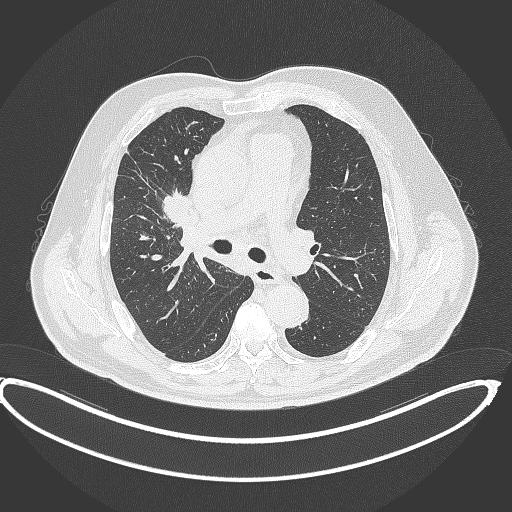
Chest CT, one axial slice. Position 254 of 390 along the scan axis. 120 kVp. Lung window (W 1500 / L -600 HU). 512 × 512 image matrix. Patient: male, 62 years. From the clinical record (not read from this slice): clinical TNM (as recorded): T1c N3 M1c.
Outlined on this slice (rectangle marked by the reading radiologist):
- lung tumour (recorded histology: adenocarcinoma): bounding box (x1, y1, x2, y2) in pixels: (159, 188, 191, 223)